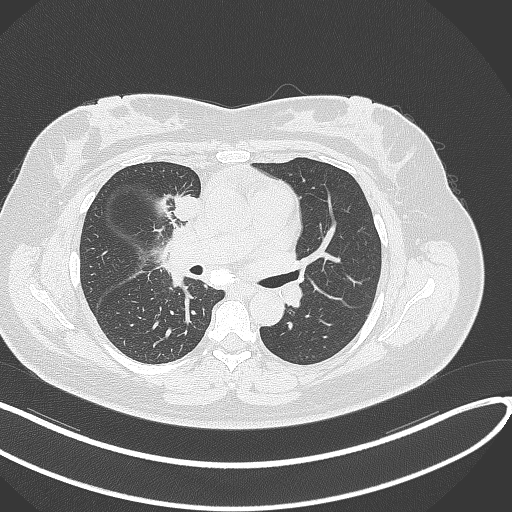
Chest CT, one axial slice; position 152 of 303 along the scan axis; reconstruction kernel B70f; 120 kVp; lung window (W 1500 / L -600 HU); 1 mm slice thickness; 512 × 512 image matrix, field of view 400 × 400 mm. Patient: female, 46 years. Case-level facts recorded for this patient, not image findings: clinical TNM (as recorded): T2a N1 M0.
Annotated regions visible in this slice (bounding box drawn by a radiologist):
- lung tumour (recorded histology: adenocarcinoma): bounding box [x1, y1, x2, y2] px = [170, 188, 202, 225]